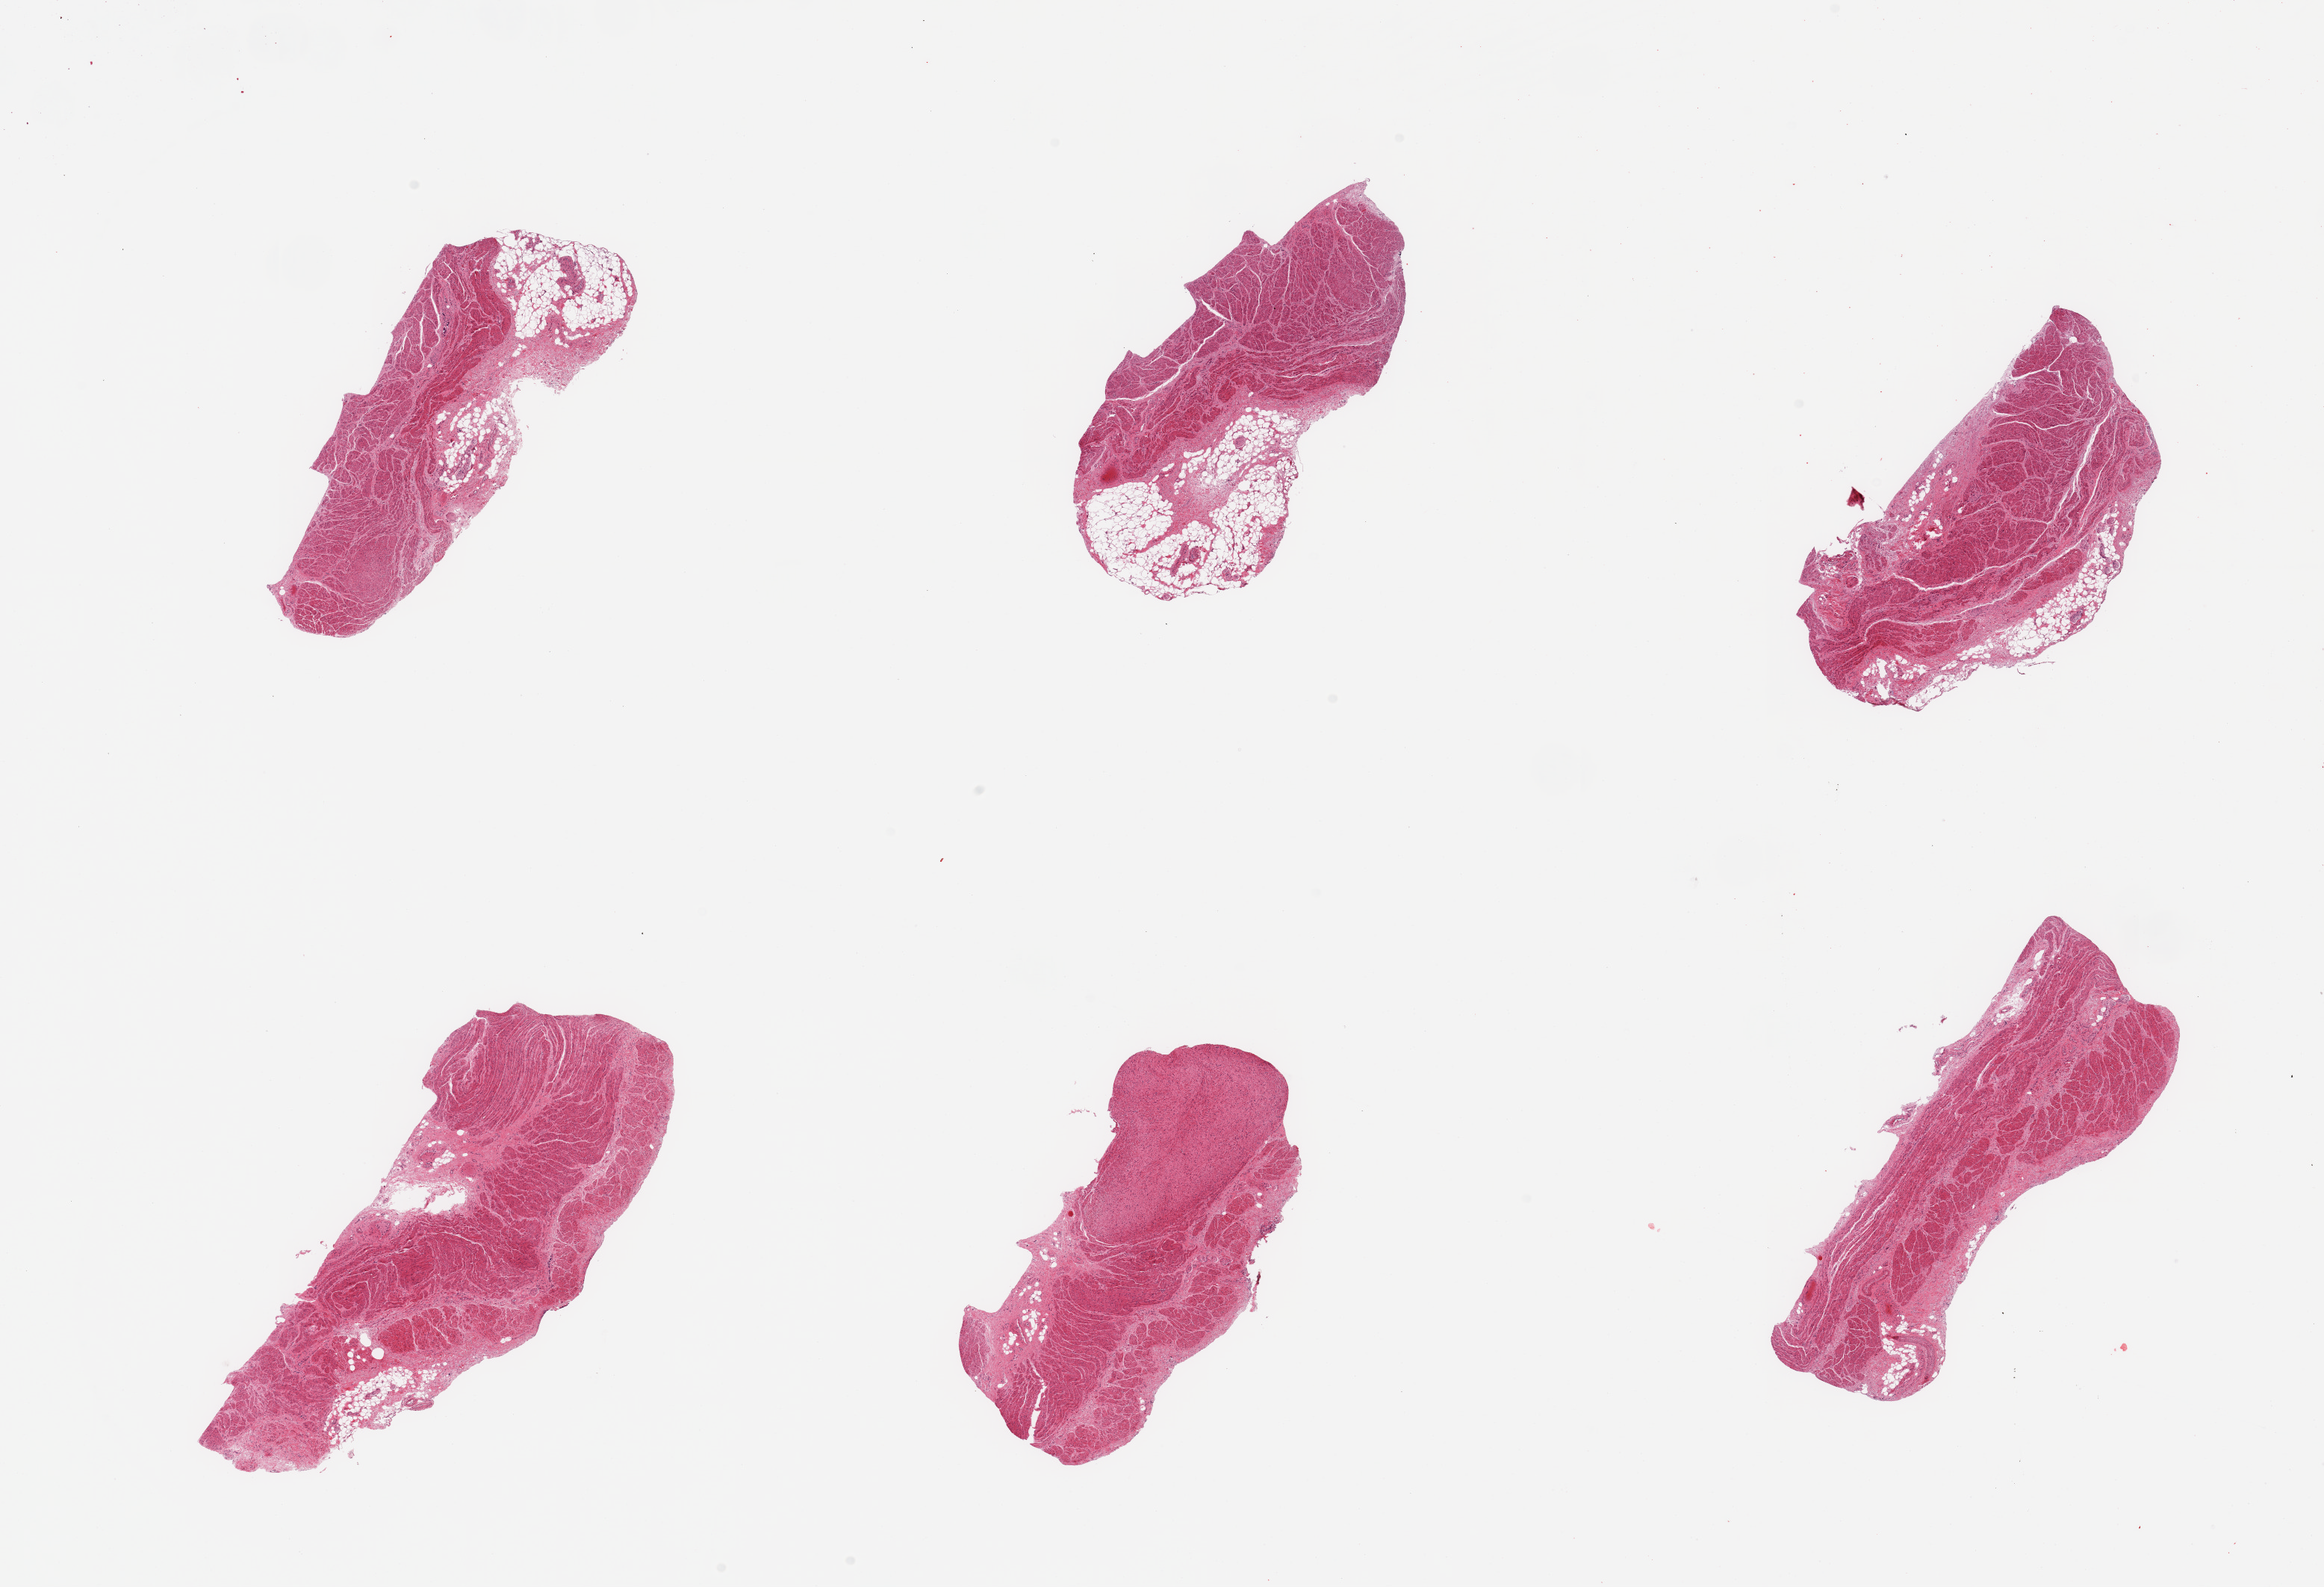
Digitized hematoxylin and eosin (H&E)-stained section — shown as a low-resolution overview of the whole scanned area (about 24.6 x 16.8 mm, slide scanned at 20x). PAXgene-fixed, paraffin-embedded tissue. Target tissue: gastroesophageal junction. Donor tissue sample. Donor sex: male.
* review note (as recorded): 6 pieces, confirmed target muscularis